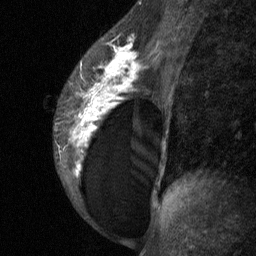
Breast MRI (dynamic contrast-enhanced), one sagittal slice; position 41 of 64 along the scan axis; dynamic contrast-enhanced study with each time point stored as its own series, time point 2 of 3 at this slice position (early post-contrast, ordered by acquisition time); 1.5 T; TE 4.8 ms, TR 27 ms; 2 mm slice thickness; 256 × 256 image matrix. Patient: female, 34 years. Case-level facts recorded for this patient, not image findings: setting: breast cancer imaged before/during neoadjuvant chemotherapy; receptor status: HR-positive, HER2-negative.
Structures marked on this image (semi-automatically segmented with operator editing):
- analysis volume of interest (the breast-tissue region the enhancement analysis was run in; not a lesion): bounding box <53,23,157,197> (left, top, right, bottom; pixels)
- tumour enhancement mask (voxels above the 90 % enhancement threshold inside the analysis volume of interest): <71,37,142,173>